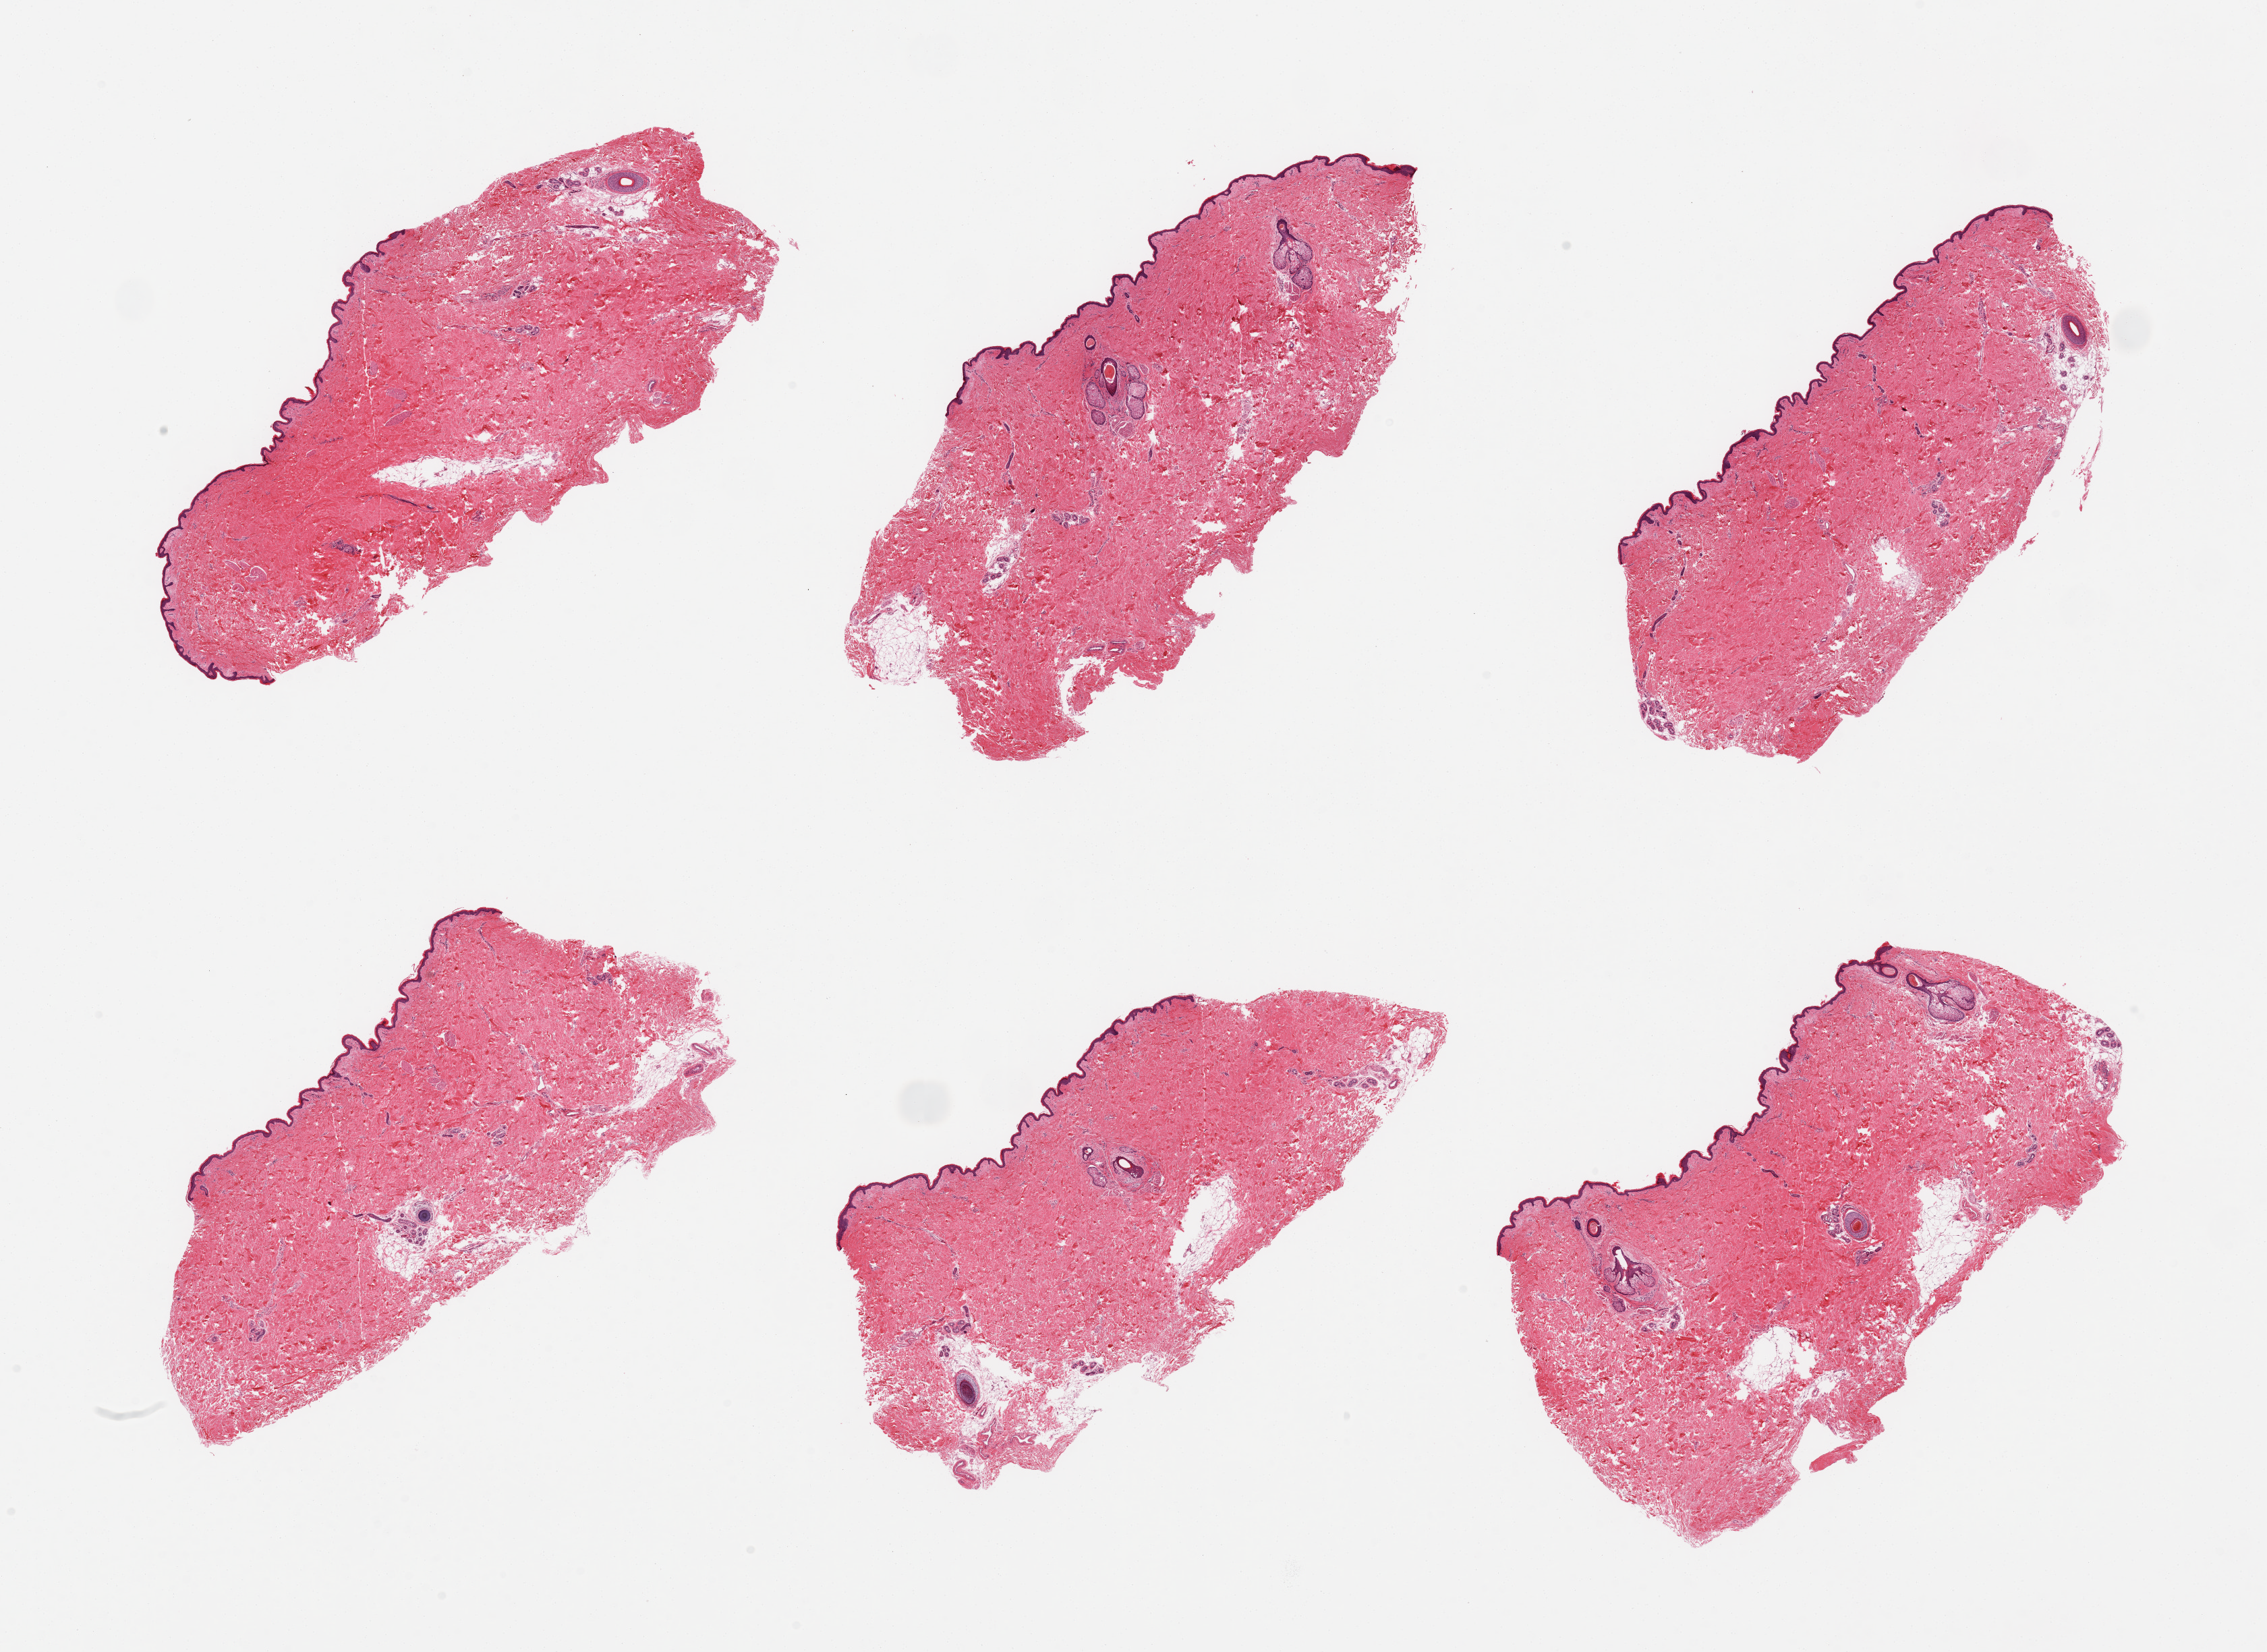
Whole-slide image, hematoxylin and eosin (H&E) stain, brightfield, shown as a low-resolution overview of the whole scanned area (about 26.6 x 19.4 mm). PAXgene-fixed, paraffin-embedded tissue. Target tissue: skin of suprapubic region. Tissue donor sample. Male donor.
Reviewer comment on this tissue sample: 6 pieces; hair-bearing skin with up to 10% internal/periadnexal fat.